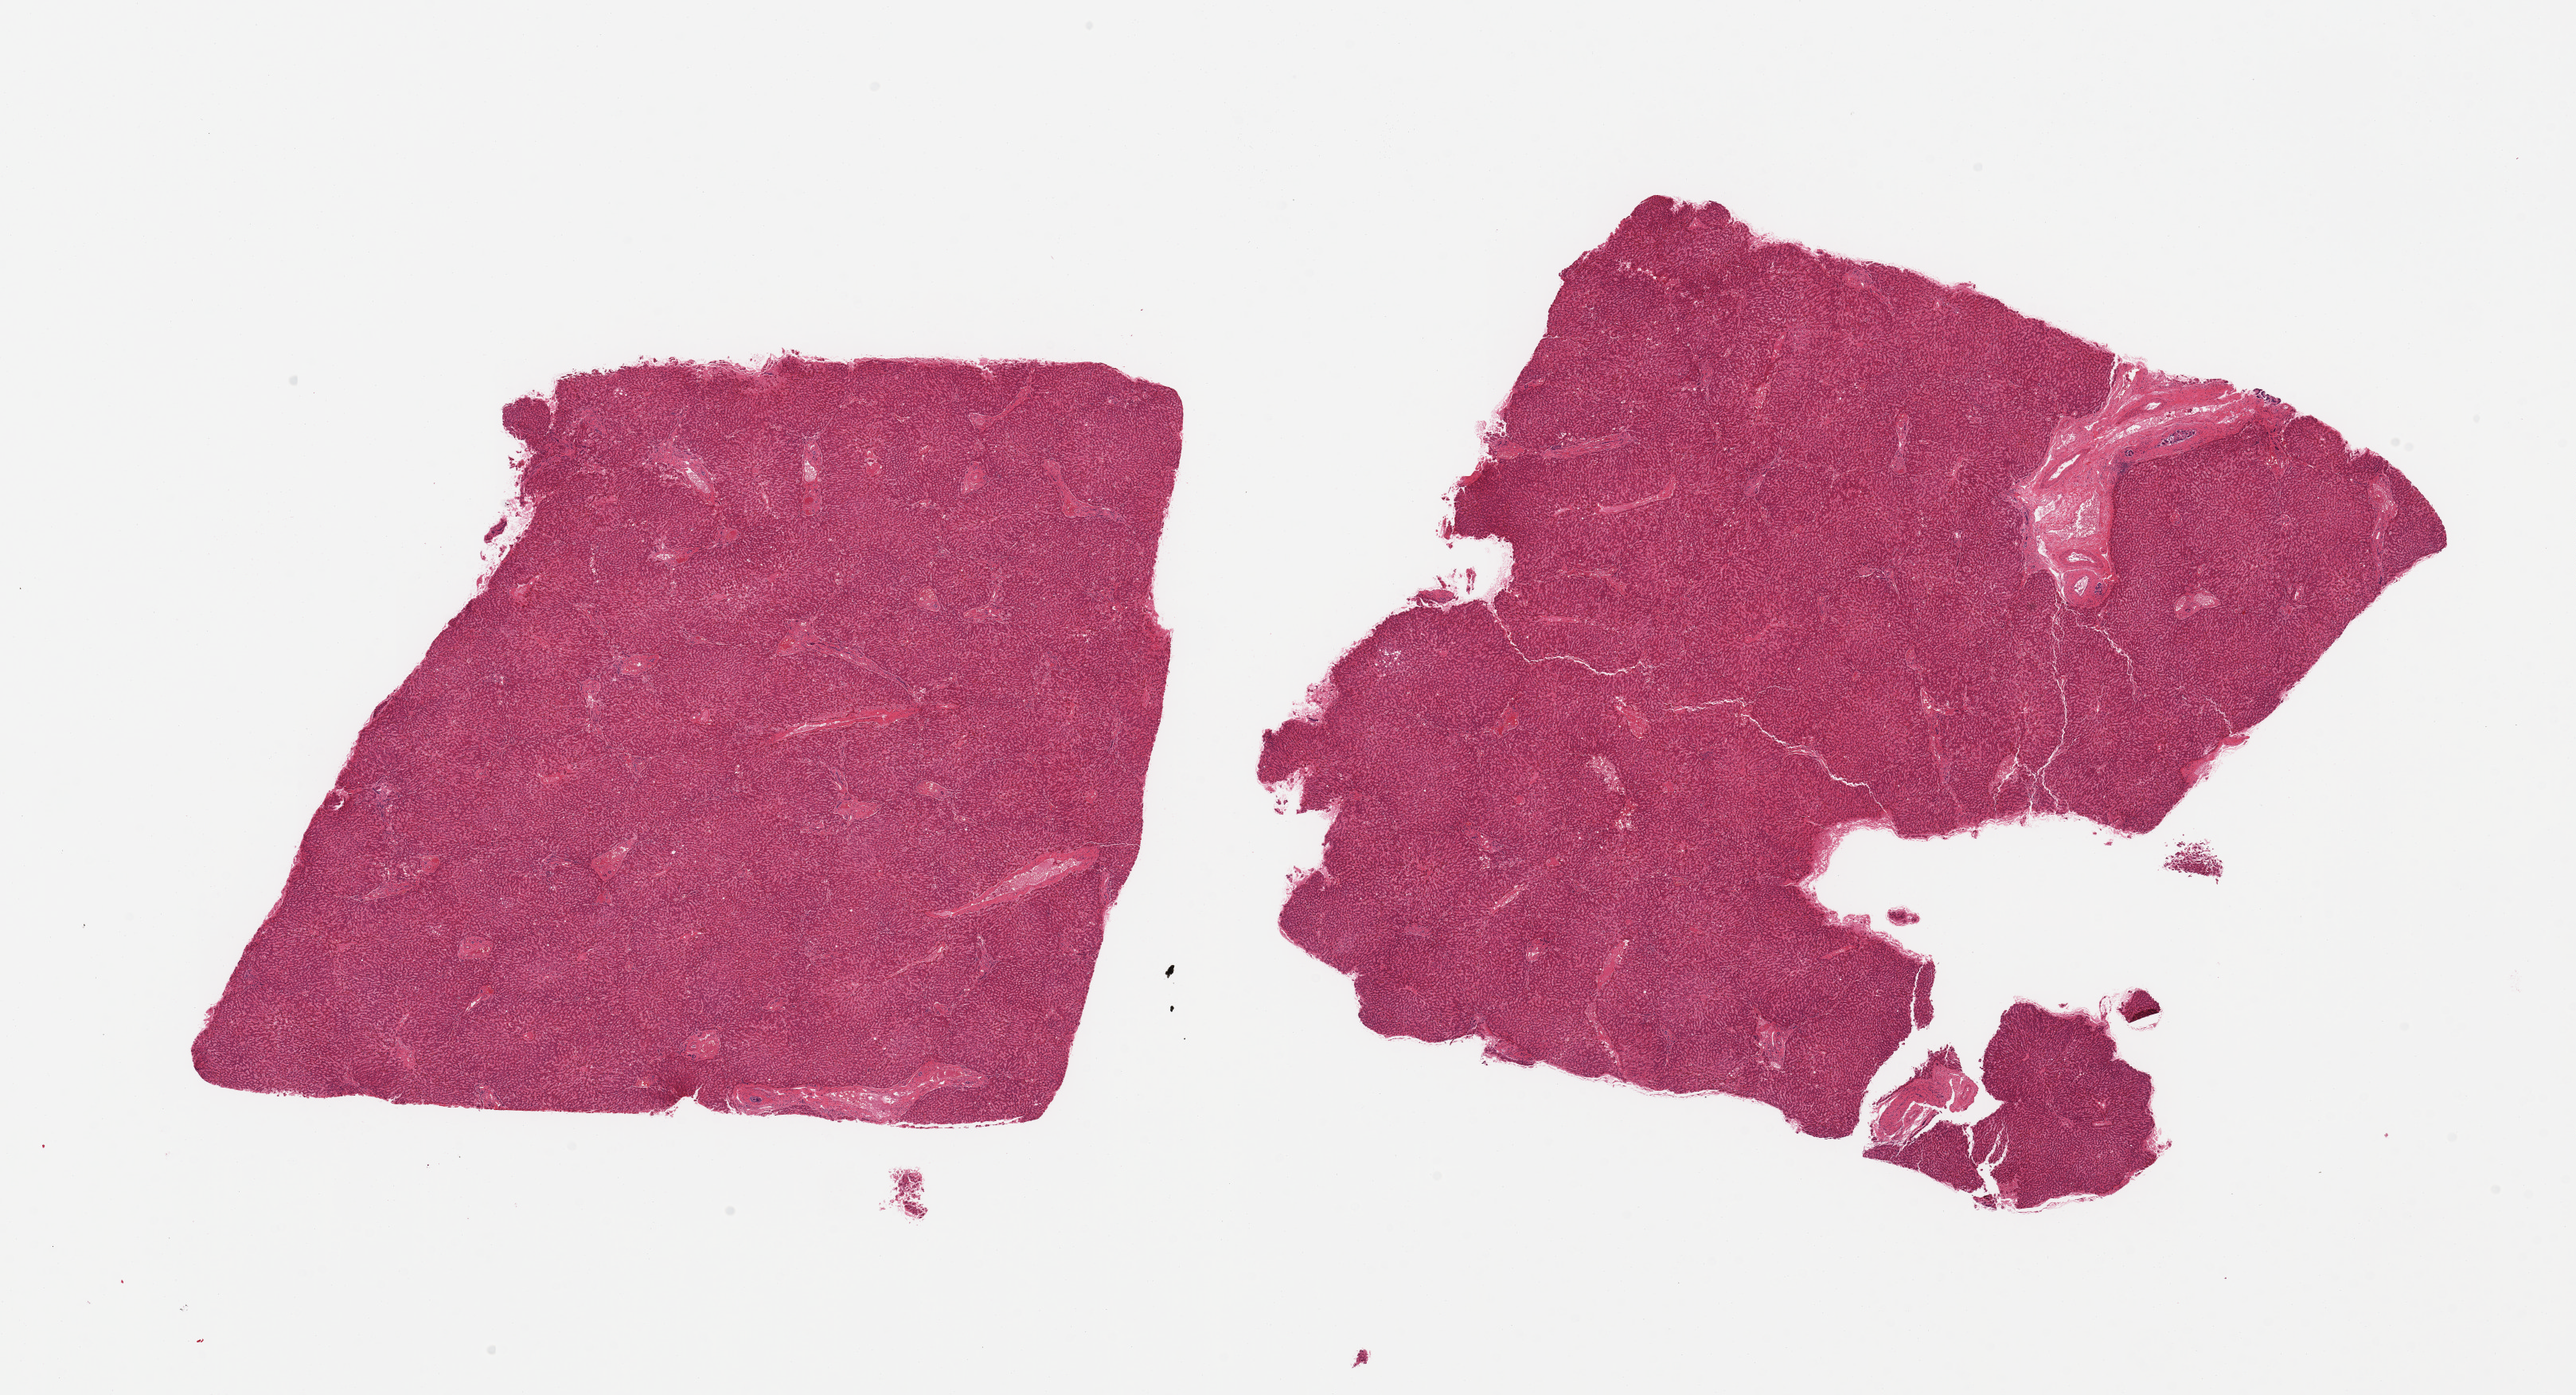
Whole-slide image, hematoxylin and eosin (H&E) stain, low-resolution overview of the scanned area, about 25.6 x 13.9 mm; PAXgene-fixed paraffin-embedded (PFPE) section; sampled site (target tissue): liver; tissue donor sample. Donor: female.
* pathologist's review note for this sample: 2 pieces; no active or chronic lesions